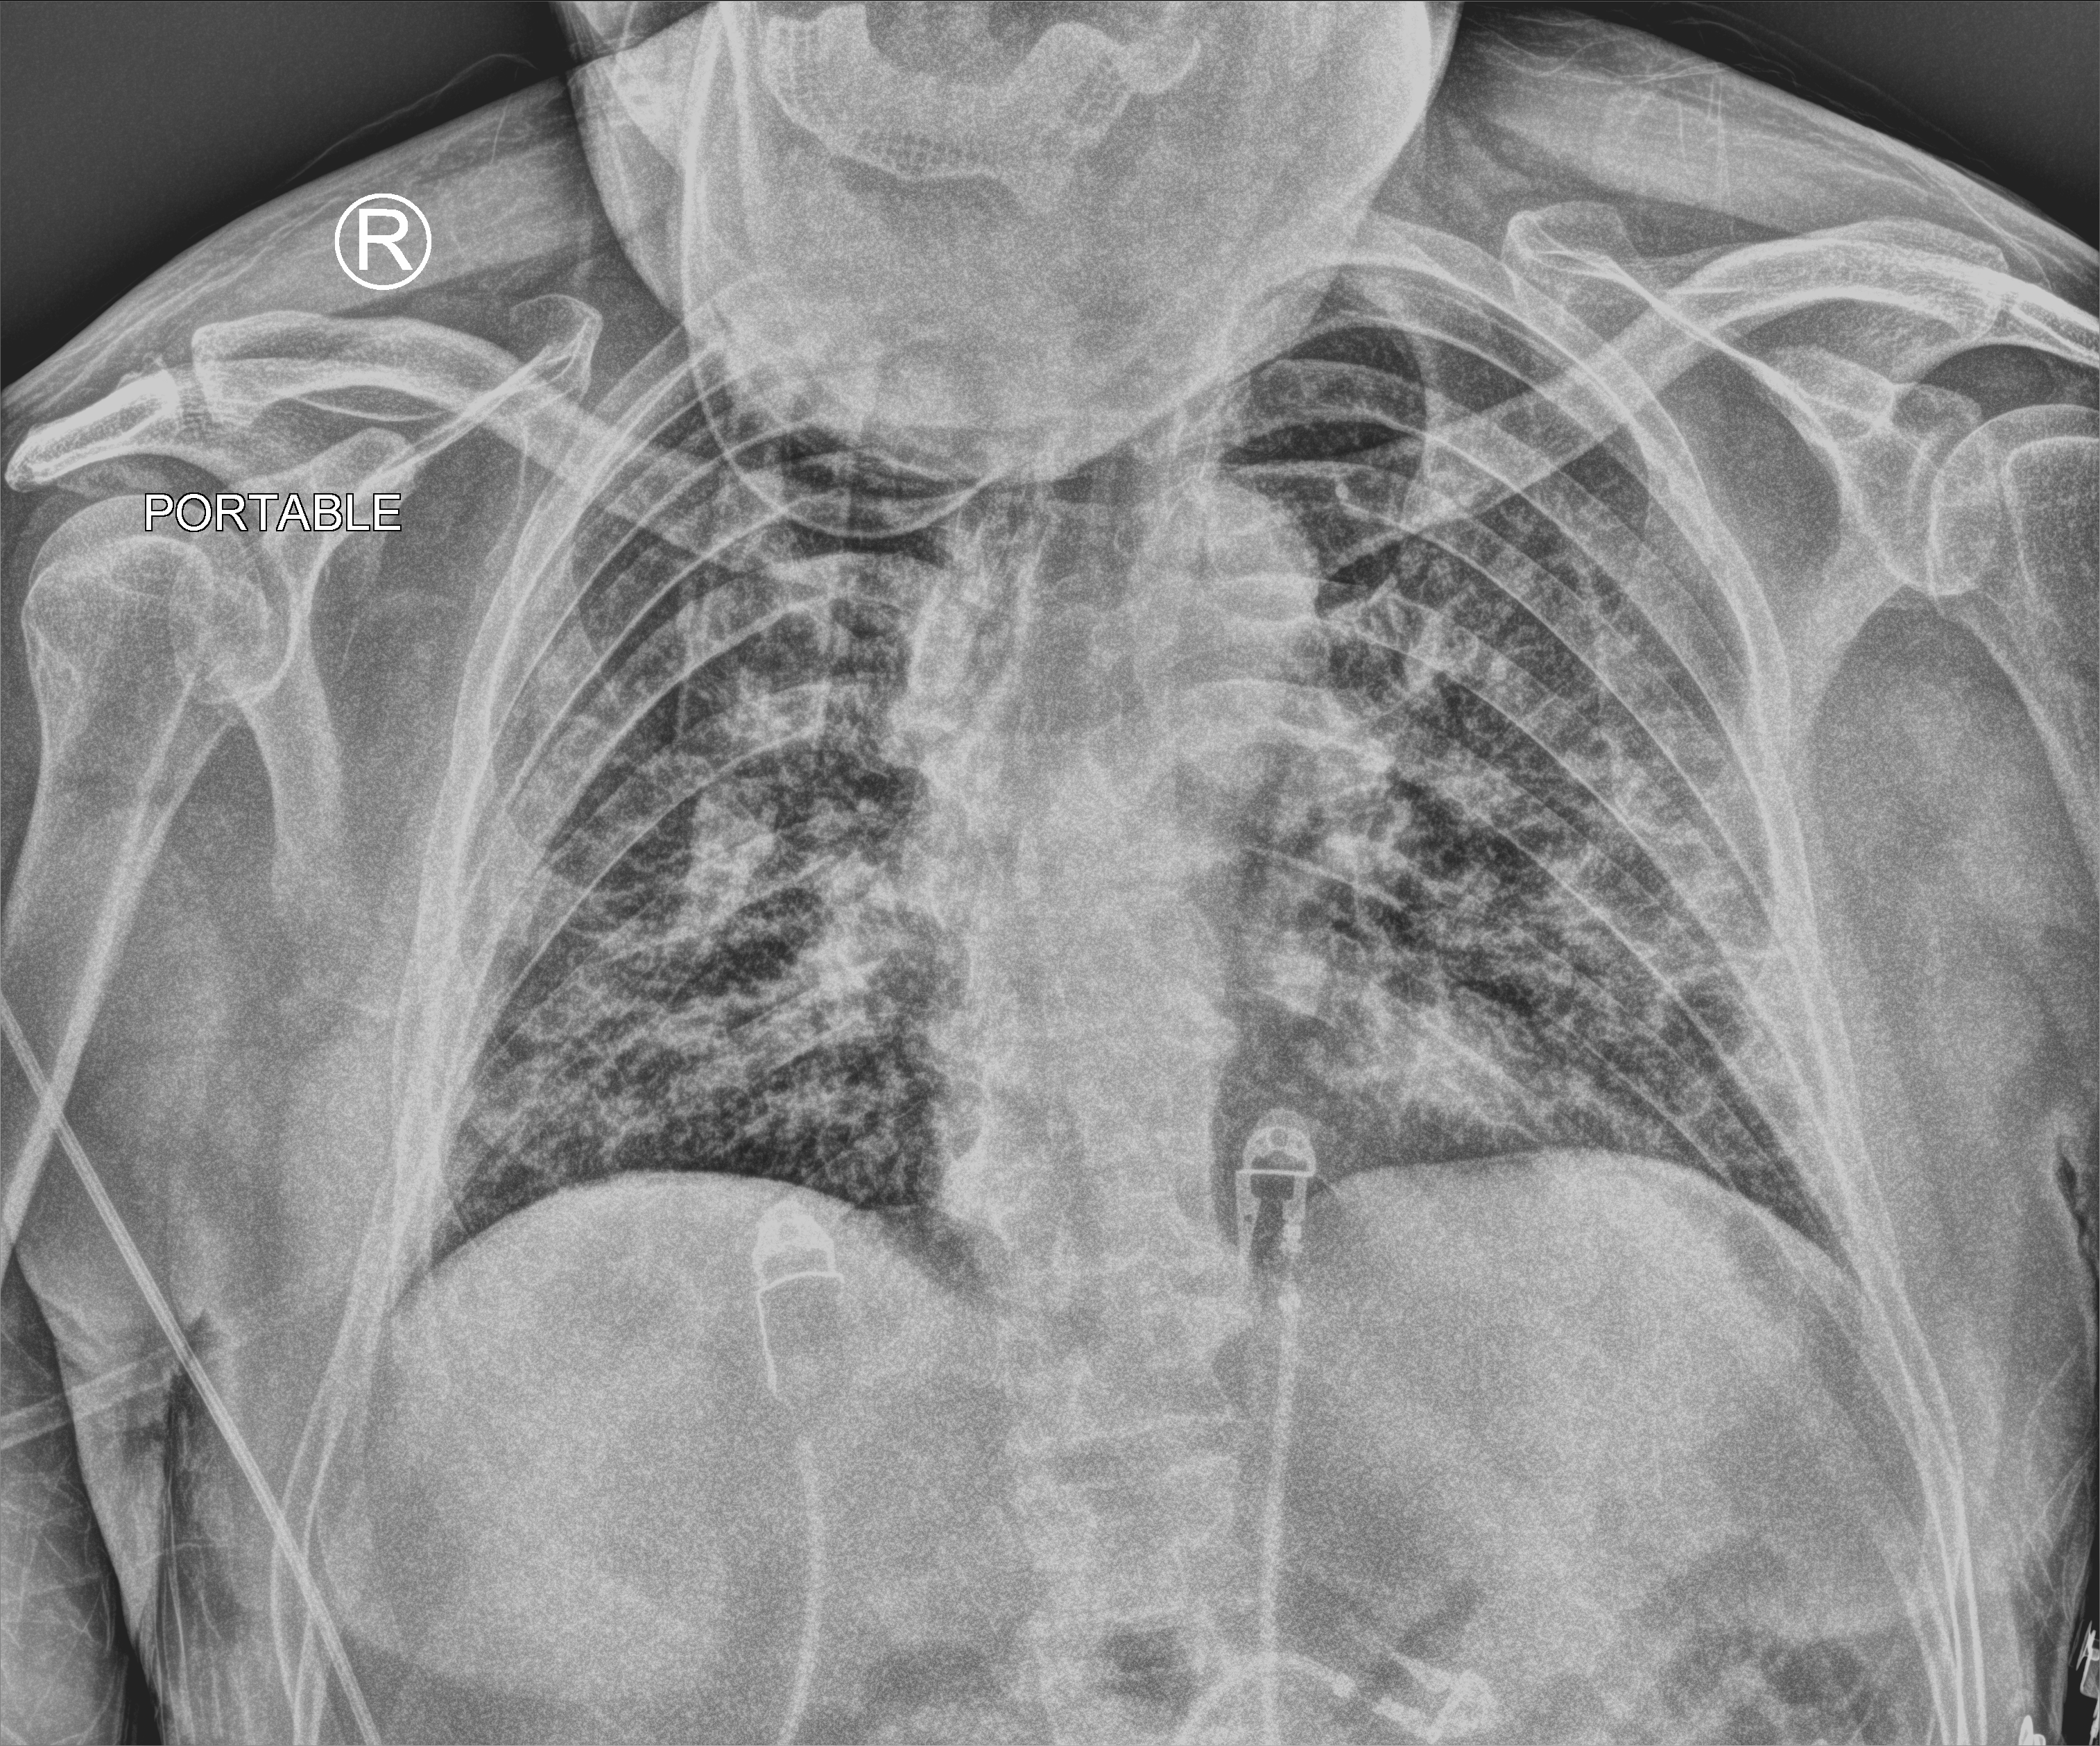
Bedside chest radiograph (computed radiography), anteroposterior (AP) projection. Patient hospitalised with COVID-19; male, aged 60–74 years.
Hospital-stay facts (about this admission, not read from this image; timing relative to this image not recorded):
- mechanically ventilated during this hospital stay: yes